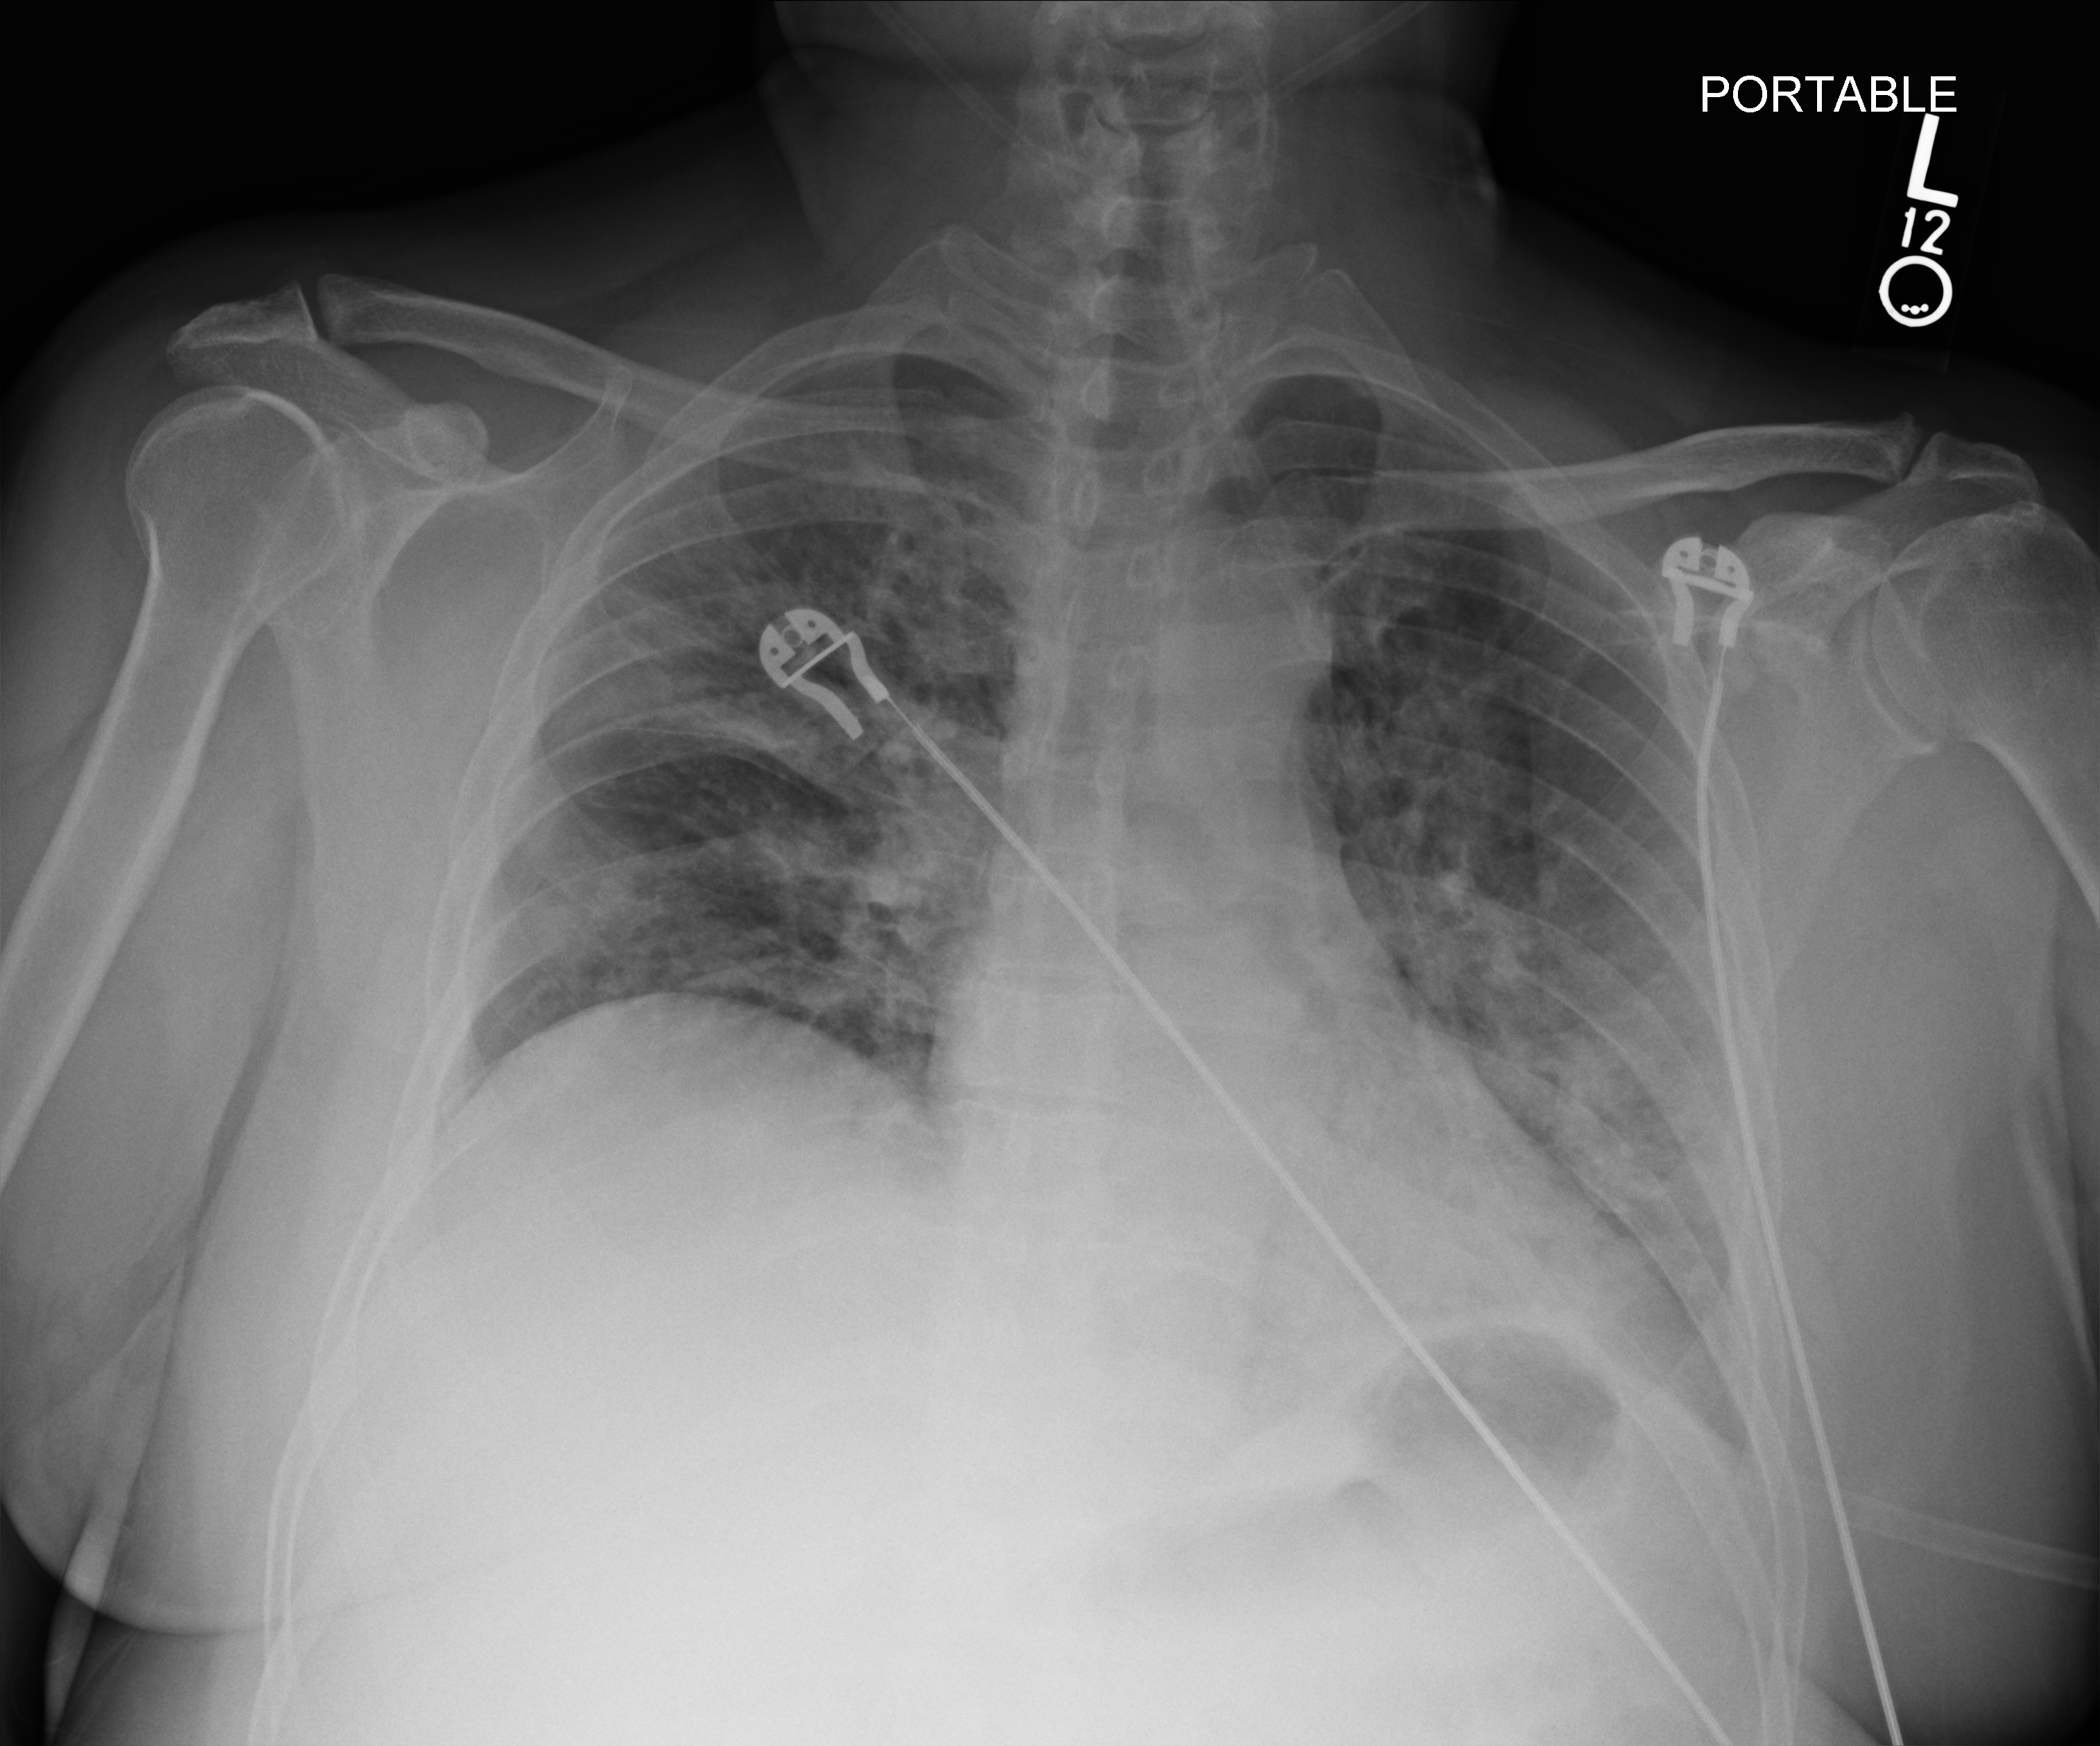
Chest X-ray (portable). Male patient hospitalised with COVID-19, age 18–59 years.
Hospital-stay facts (about this admission, not read from this image; timing relative to this image not recorded):
- mechanically ventilated during this hospital stay: yes